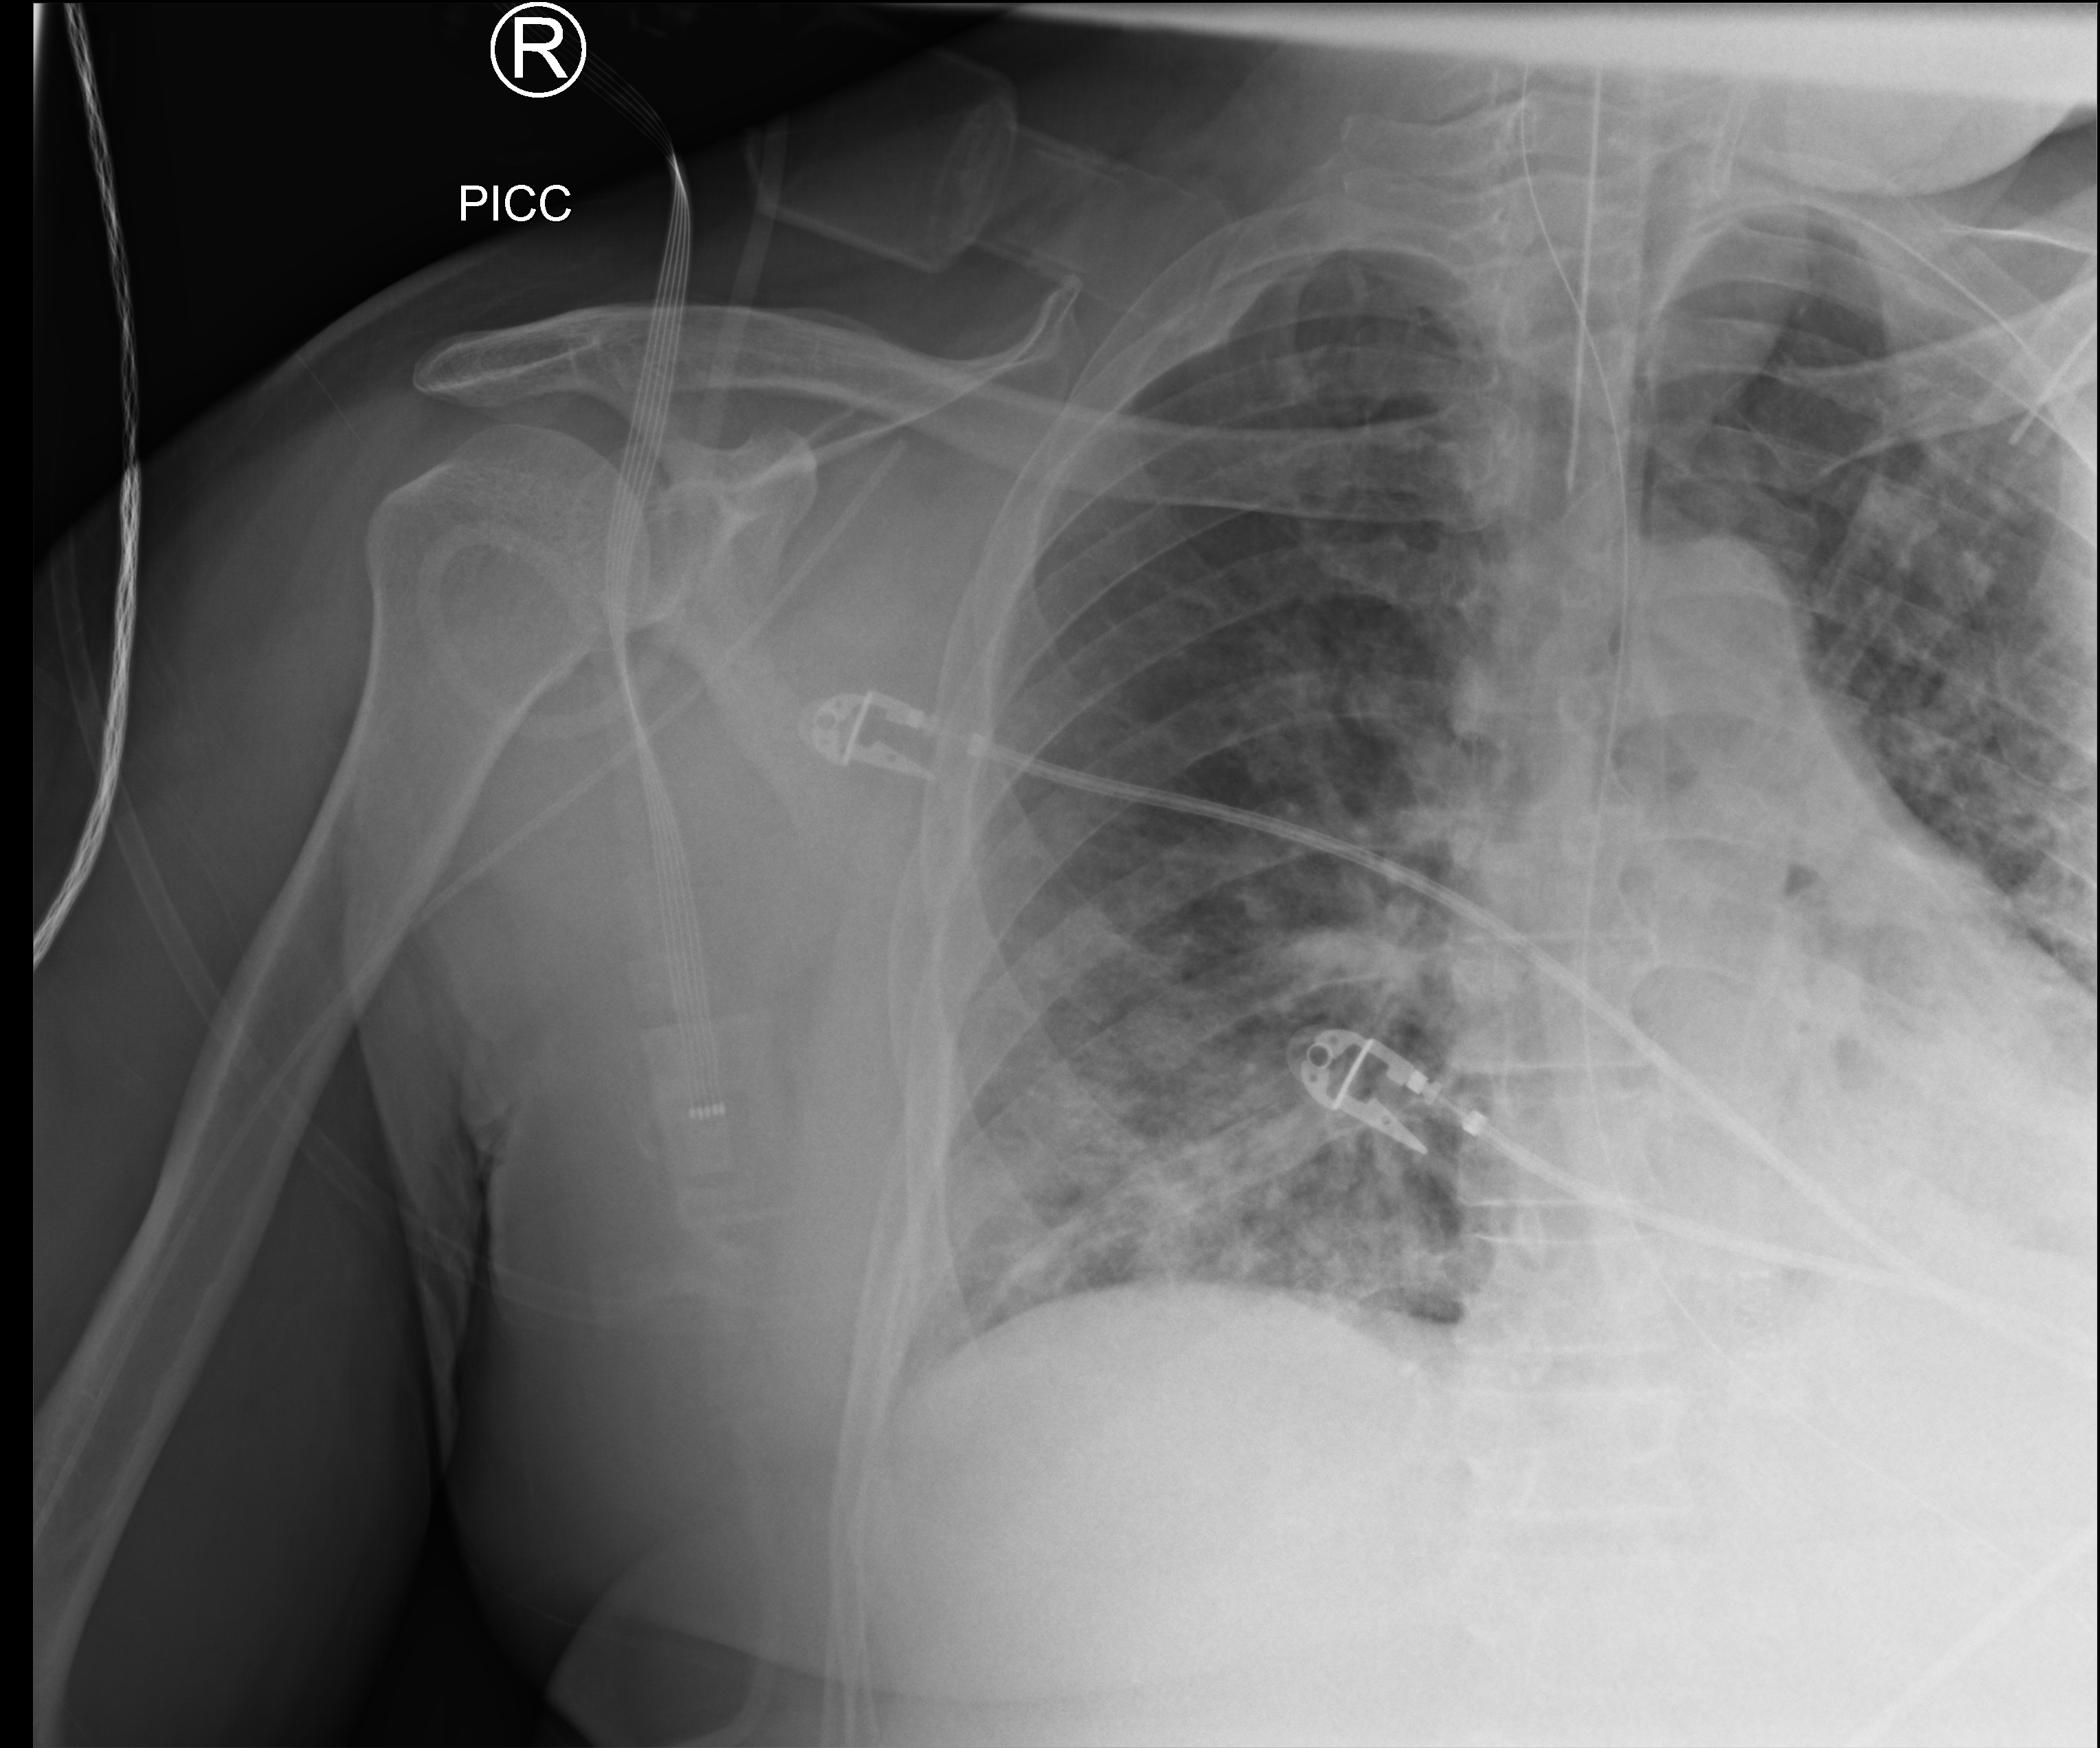
Chest X-ray (portable); anteroposterior (AP) projection. Male patient hospitalised with COVID-19, age 18–59 years.
From the hospital-stay record, not from the radiograph (when in the stay this image was taken is not recorded):
- chronic kidney disease (admission record): no
- mechanically ventilated during this hospital stay: yes